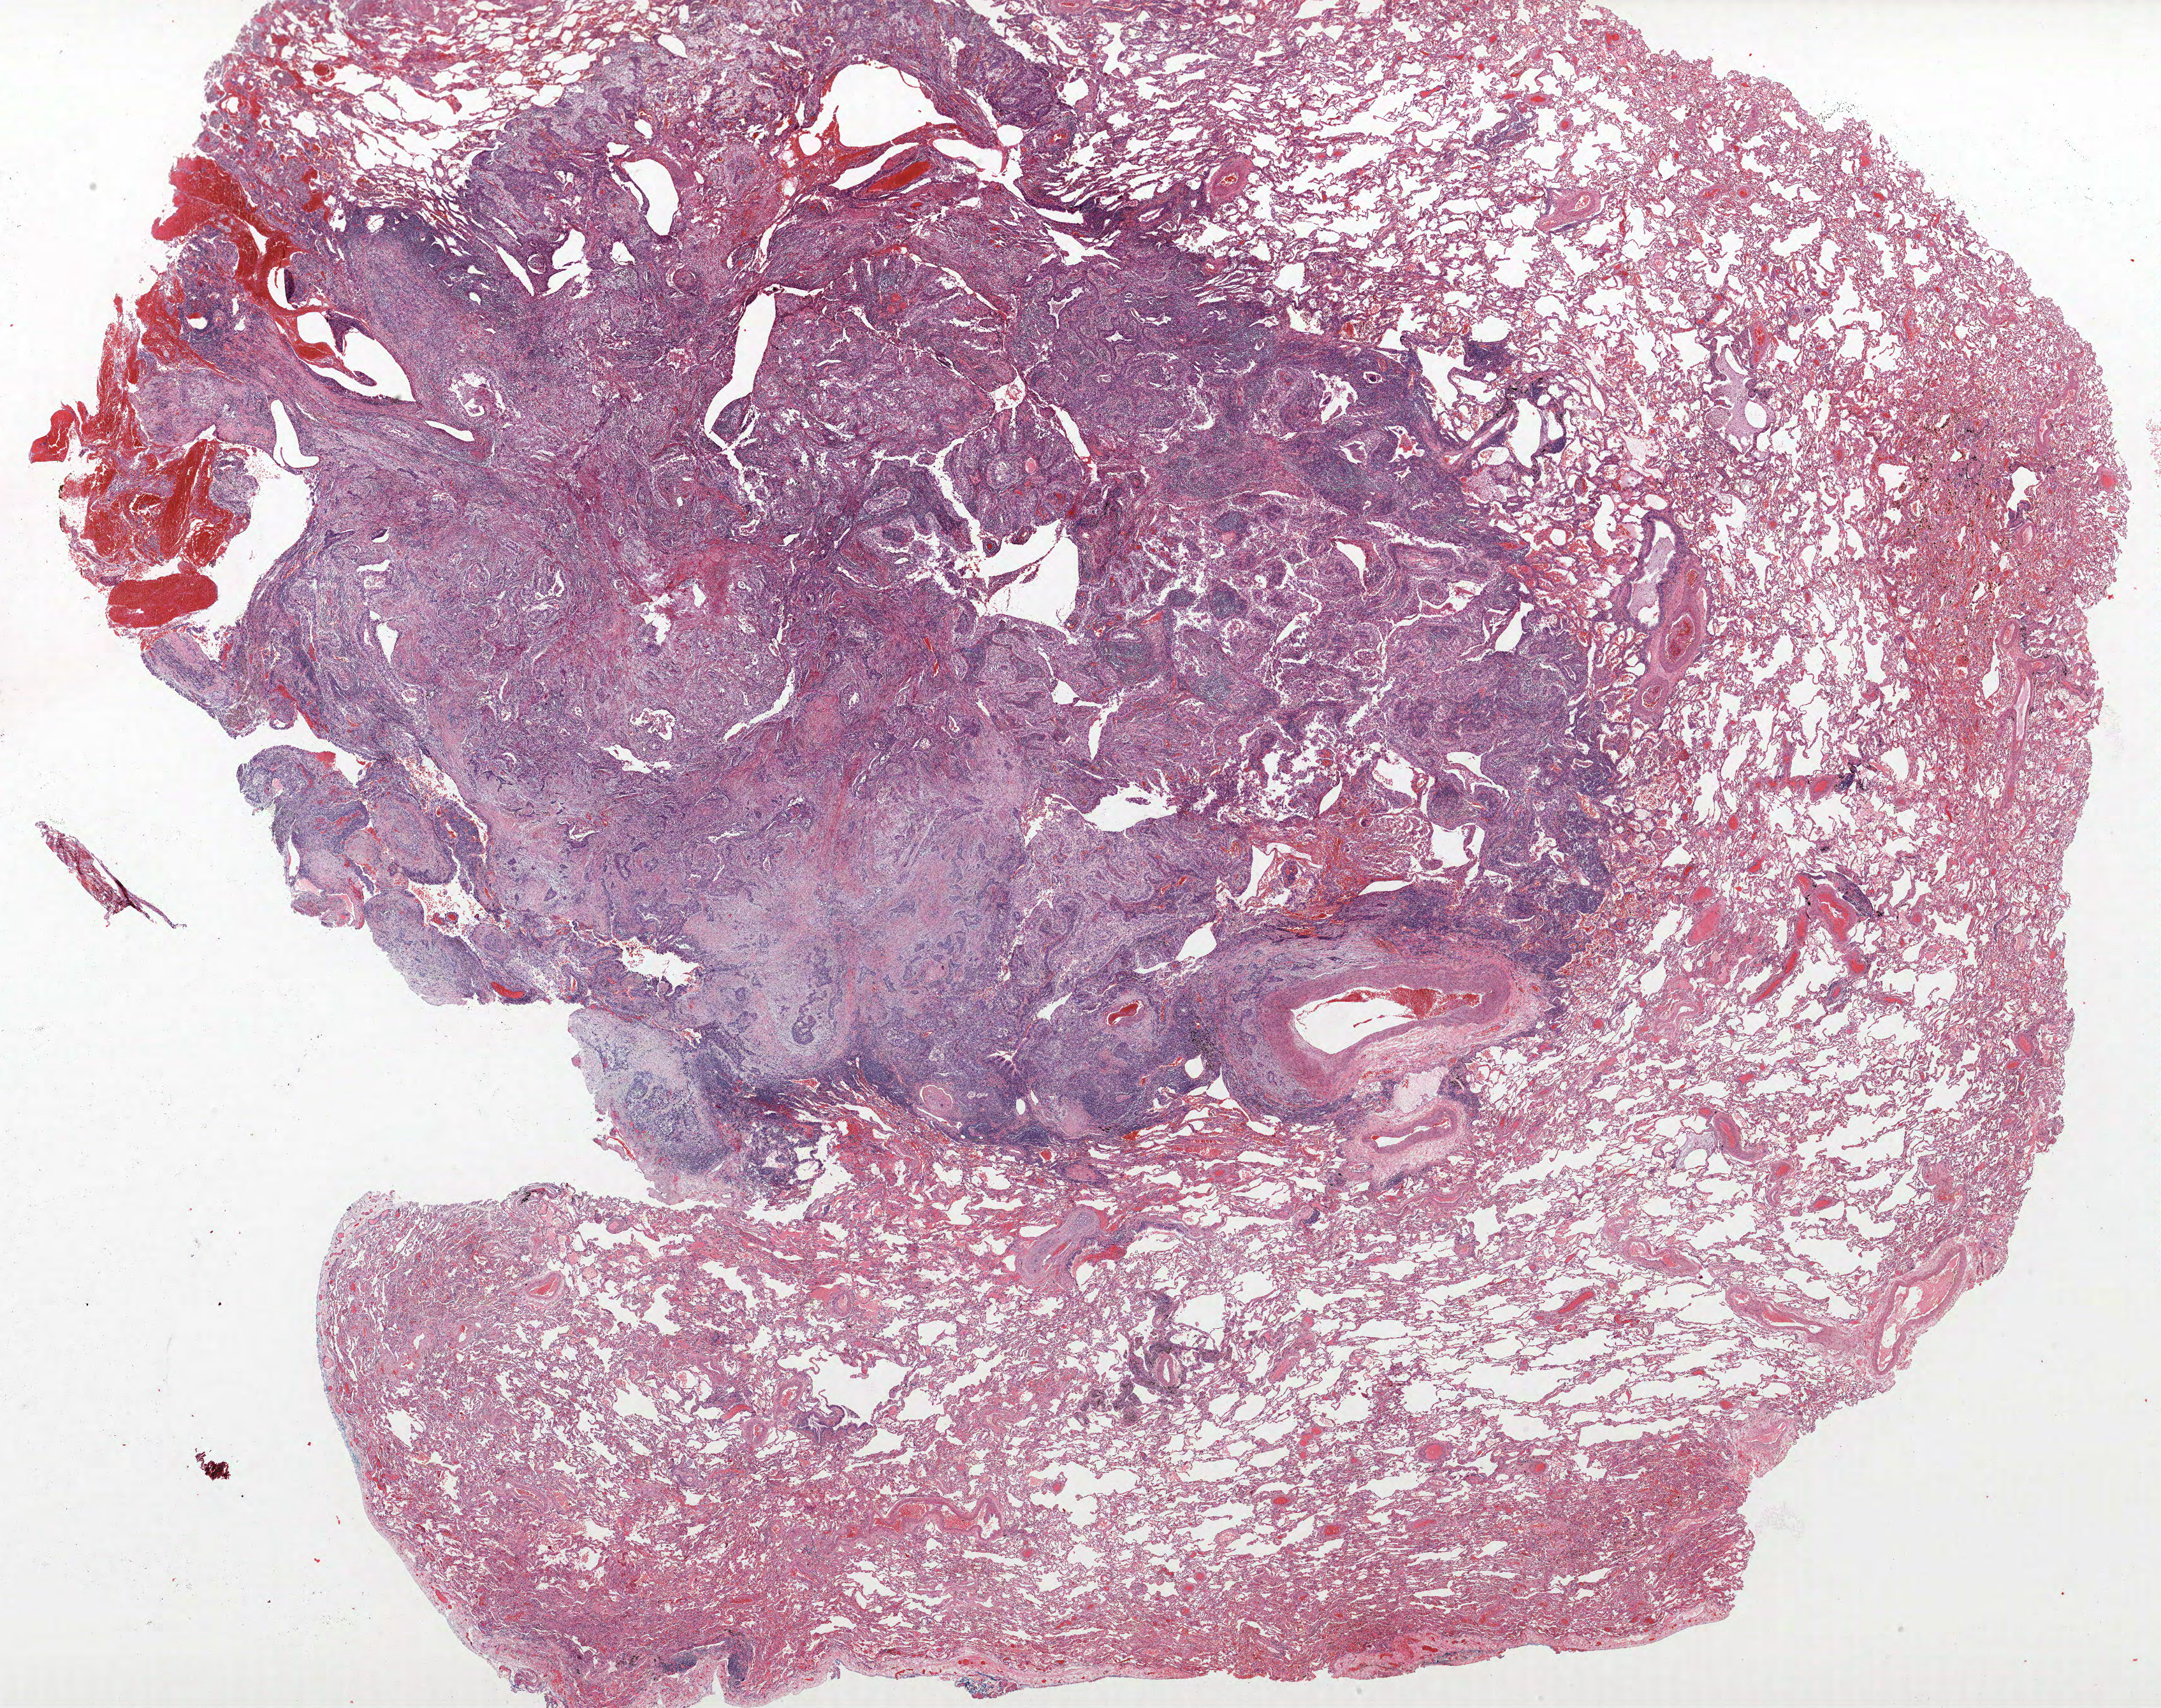
H&E-stained whole-slide image, low-resolution overview of the scanned area, about 27.1 x 21.4 mm; formalin-fixed paraffin-embedded (FFPE) section; lung tissue. Male patient, aged 57 at enrolment. Grade: moderately differentiated (G2).
Stage (AJCC 6th edition): IA. Primary tumour location (clinical record): left lower lobe. Tumour size (pathology): 22 mm. Participant's lung-cancer diagnosis: Squamous cell carcinoma, NOS (ICD-O-3 8070/3).